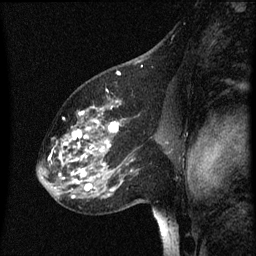
Breast MRI (dynamic contrast-enhanced), one sagittal slice; position 39 of 60 along the scan axis; dynamic contrast-enhanced series, image 2 of 3 at this slice position (ordered by acquisition); 1.5 T; TE 4.2 ms, TR 8 ms; 2 mm slice thickness; 256 × 256 image matrix, field of view 200 × 200 mm. Female patient, age 60 years.
Outlined on this slice (semi-automatically segmented with operator editing):
- analysis volume of interest (the breast-tissue region the enhancement analysis was run in; not a lesion): bounding box <49,100,158,197> (left, top, right, bottom; pixels)
- tumour enhancement mask (voxels above the 70 % enhancement threshold inside the analysis volume of interest): <60,102,134,197>